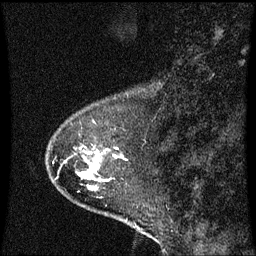
Breast MRI (dynamic contrast-enhanced), one sagittal slice. Slice 15 of 60 in the series (ordered by position). Dynamic contrast-enhanced series, image 2 of 3 at this slice position (ordered by acquisition). 1.5 T. TE 4.2 ms, TR 8.9 ms. 2 mm slice thickness. 256 × 256 image matrix, field of view 200 × 200 mm. Female patient, age 53 years. Case-level facts recorded for this patient, not image findings: setting: breast cancer imaged before/during neoadjuvant chemotherapy; receptor status: HR-positive, HER2-negative.
Structures marked on this image (semi-automatic segmentation, software-assisted and operator-edited):
- analysis volume of interest (the breast-tissue region the enhancement analysis was run in; not a lesion): bounding box [x1, y1, x2, y2] px = [54, 148, 139, 217]
- tumour enhancement mask (voxels above the 70 % enhancement threshold inside the analysis volume of interest): [94, 164, 99, 167]